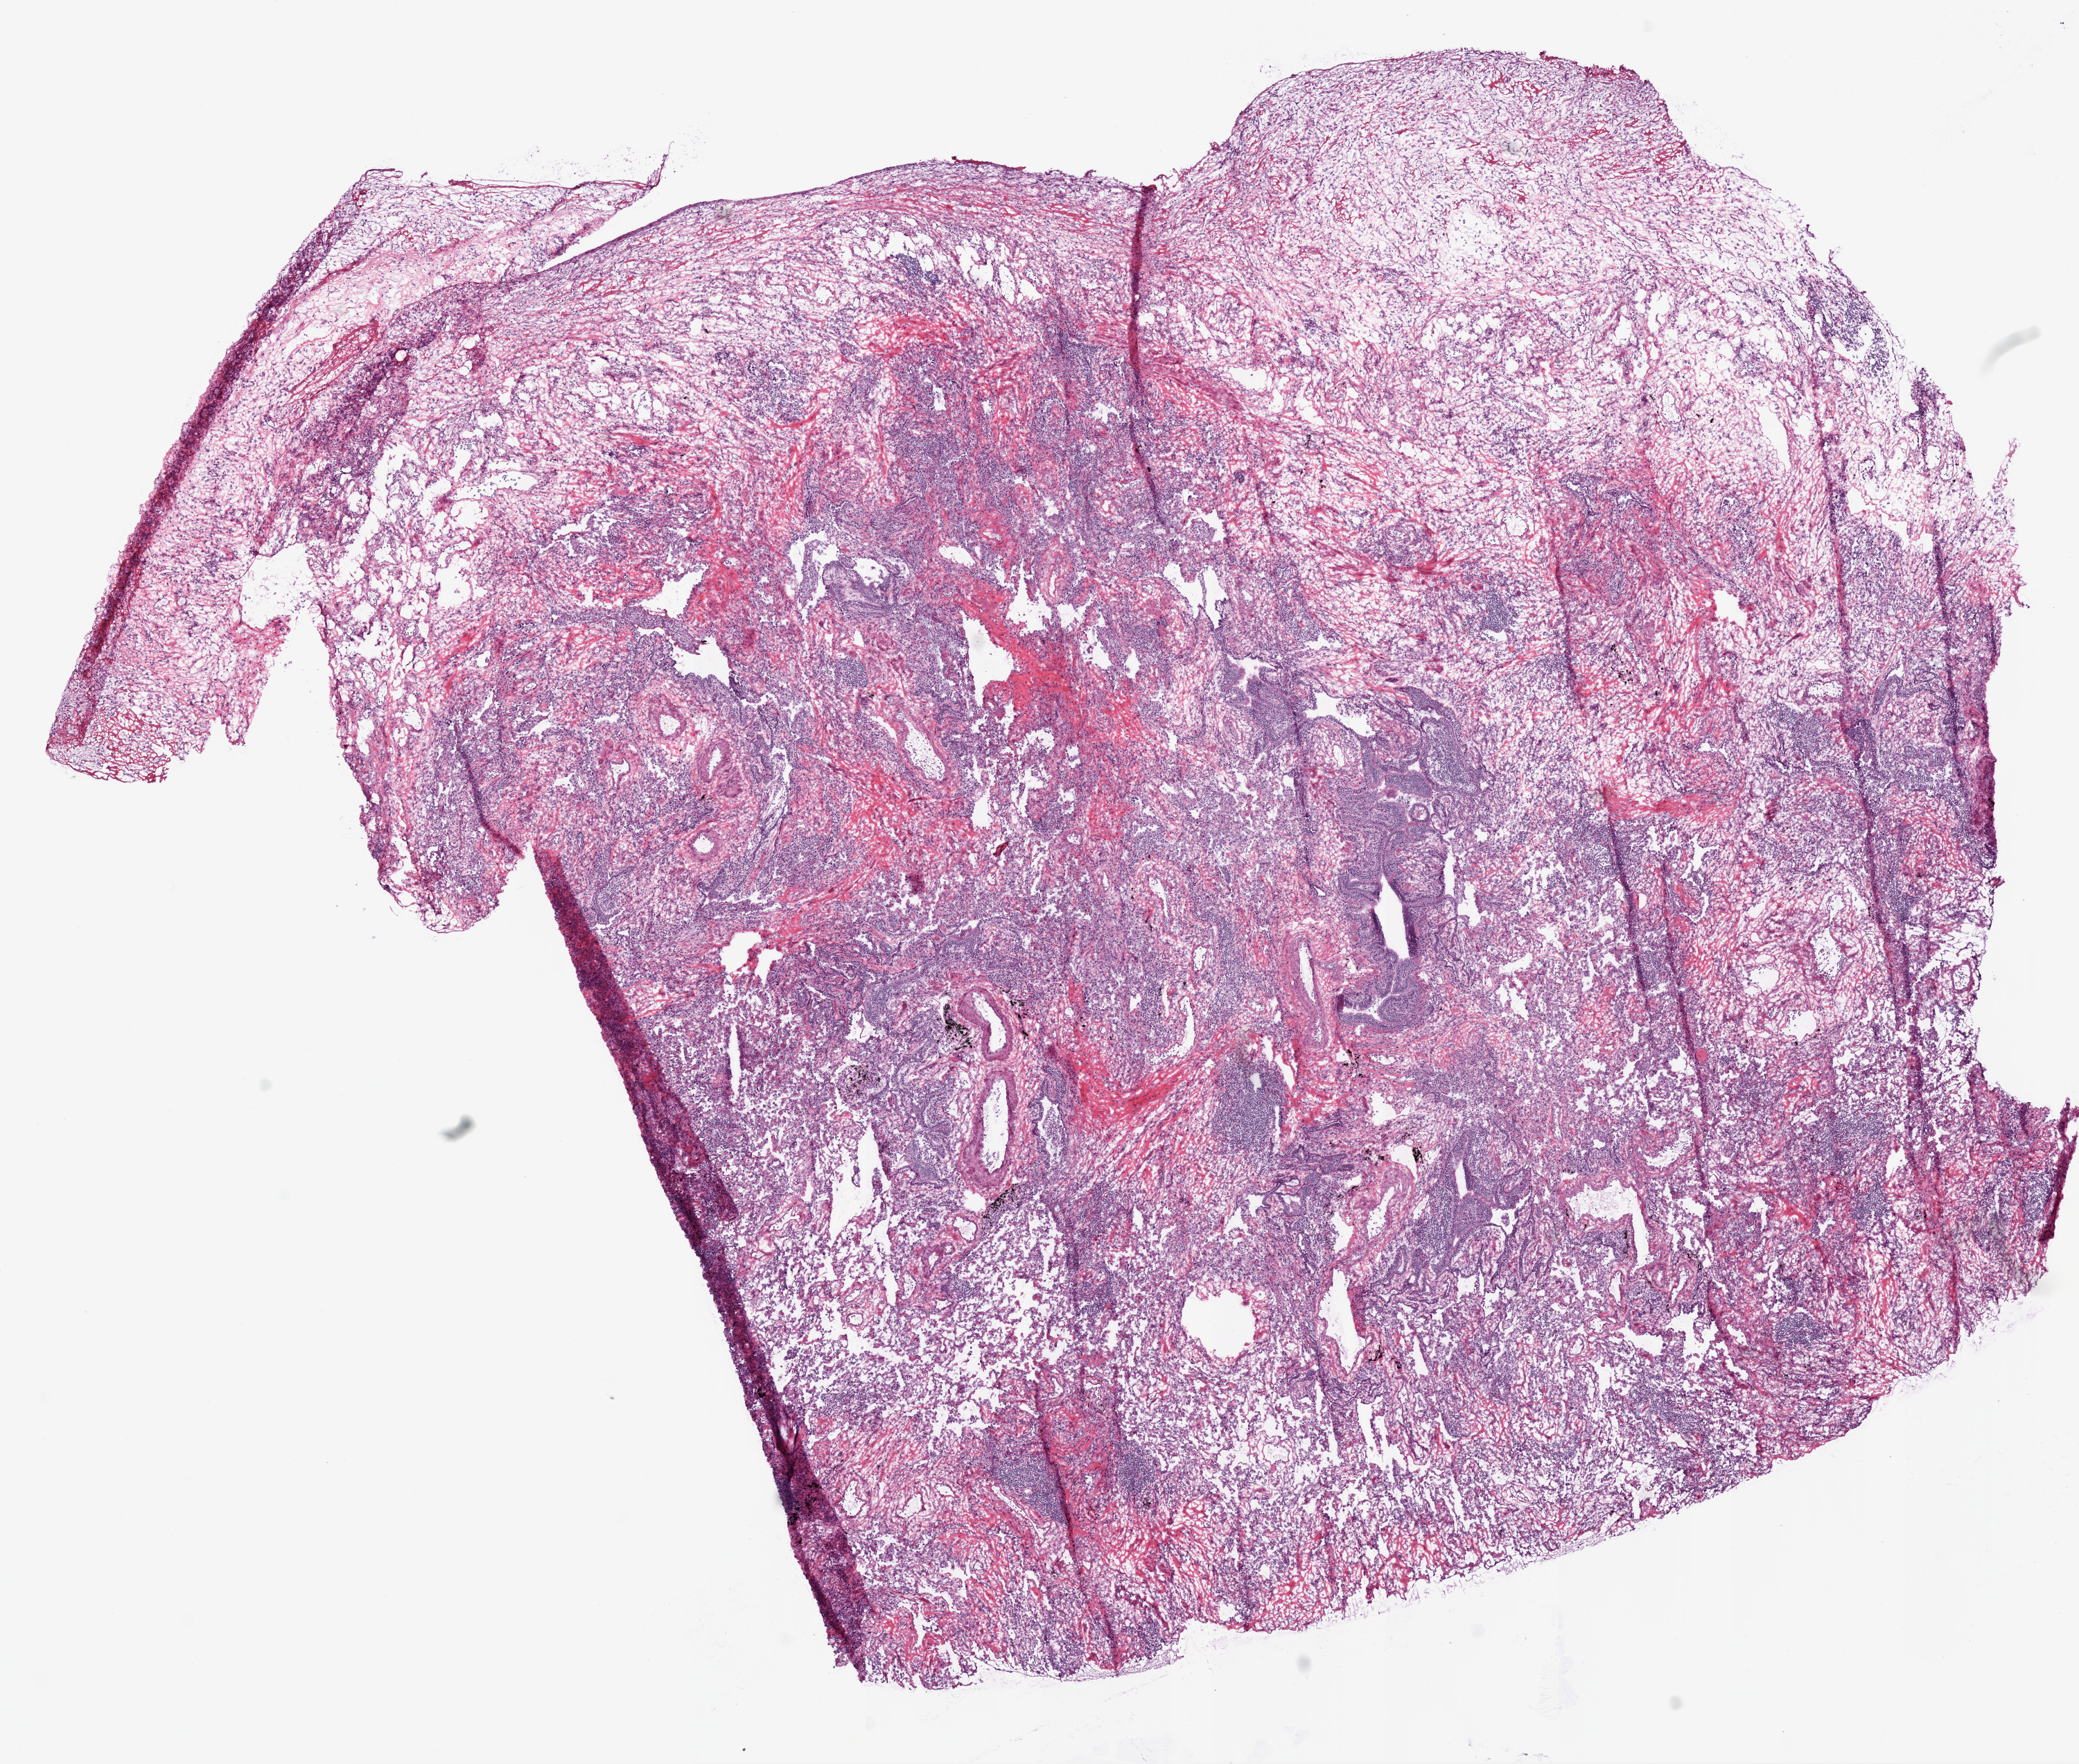
Digitized H&E-stained tissue section (whole slide) — shown as a low-resolution overview of the whole scanned area (about 12.0 x 10.2 mm, from a 20x scan). Frozen section. Sample: solid tissue normal (non-tumour tissue), lung. Male, age 69 years at initial diagnosis.
• this section: solid tissue normal sample (biorepository sample class)
• patient diagnosis: Squamous cell carcinoma, NOS (lower lobe, lung)